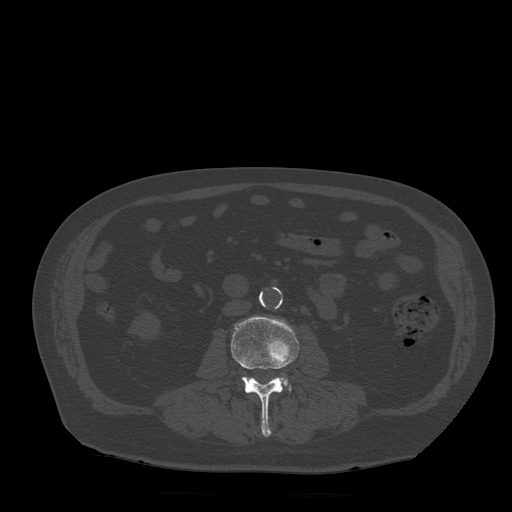
CT including the spine, one axial slice. Slice 138 of 522 in the series (ordered by position). Bone window (W 1800 / L 400 HU). 1.25 mm slice thickness. 512 × 512 image matrix, field of view 420 × 420 mm. Patient age 72 years. From the clinical record (not read from this slice): primary cancer: prostate.
Structures marked on this image (semi-automatic segmentation, software-assisted and operator-edited):
- L3 vertebra: bounding box [x1, y1, x2, y2] px = [231, 316, 300, 437]
- L4 vertebra: [246, 377, 291, 391]